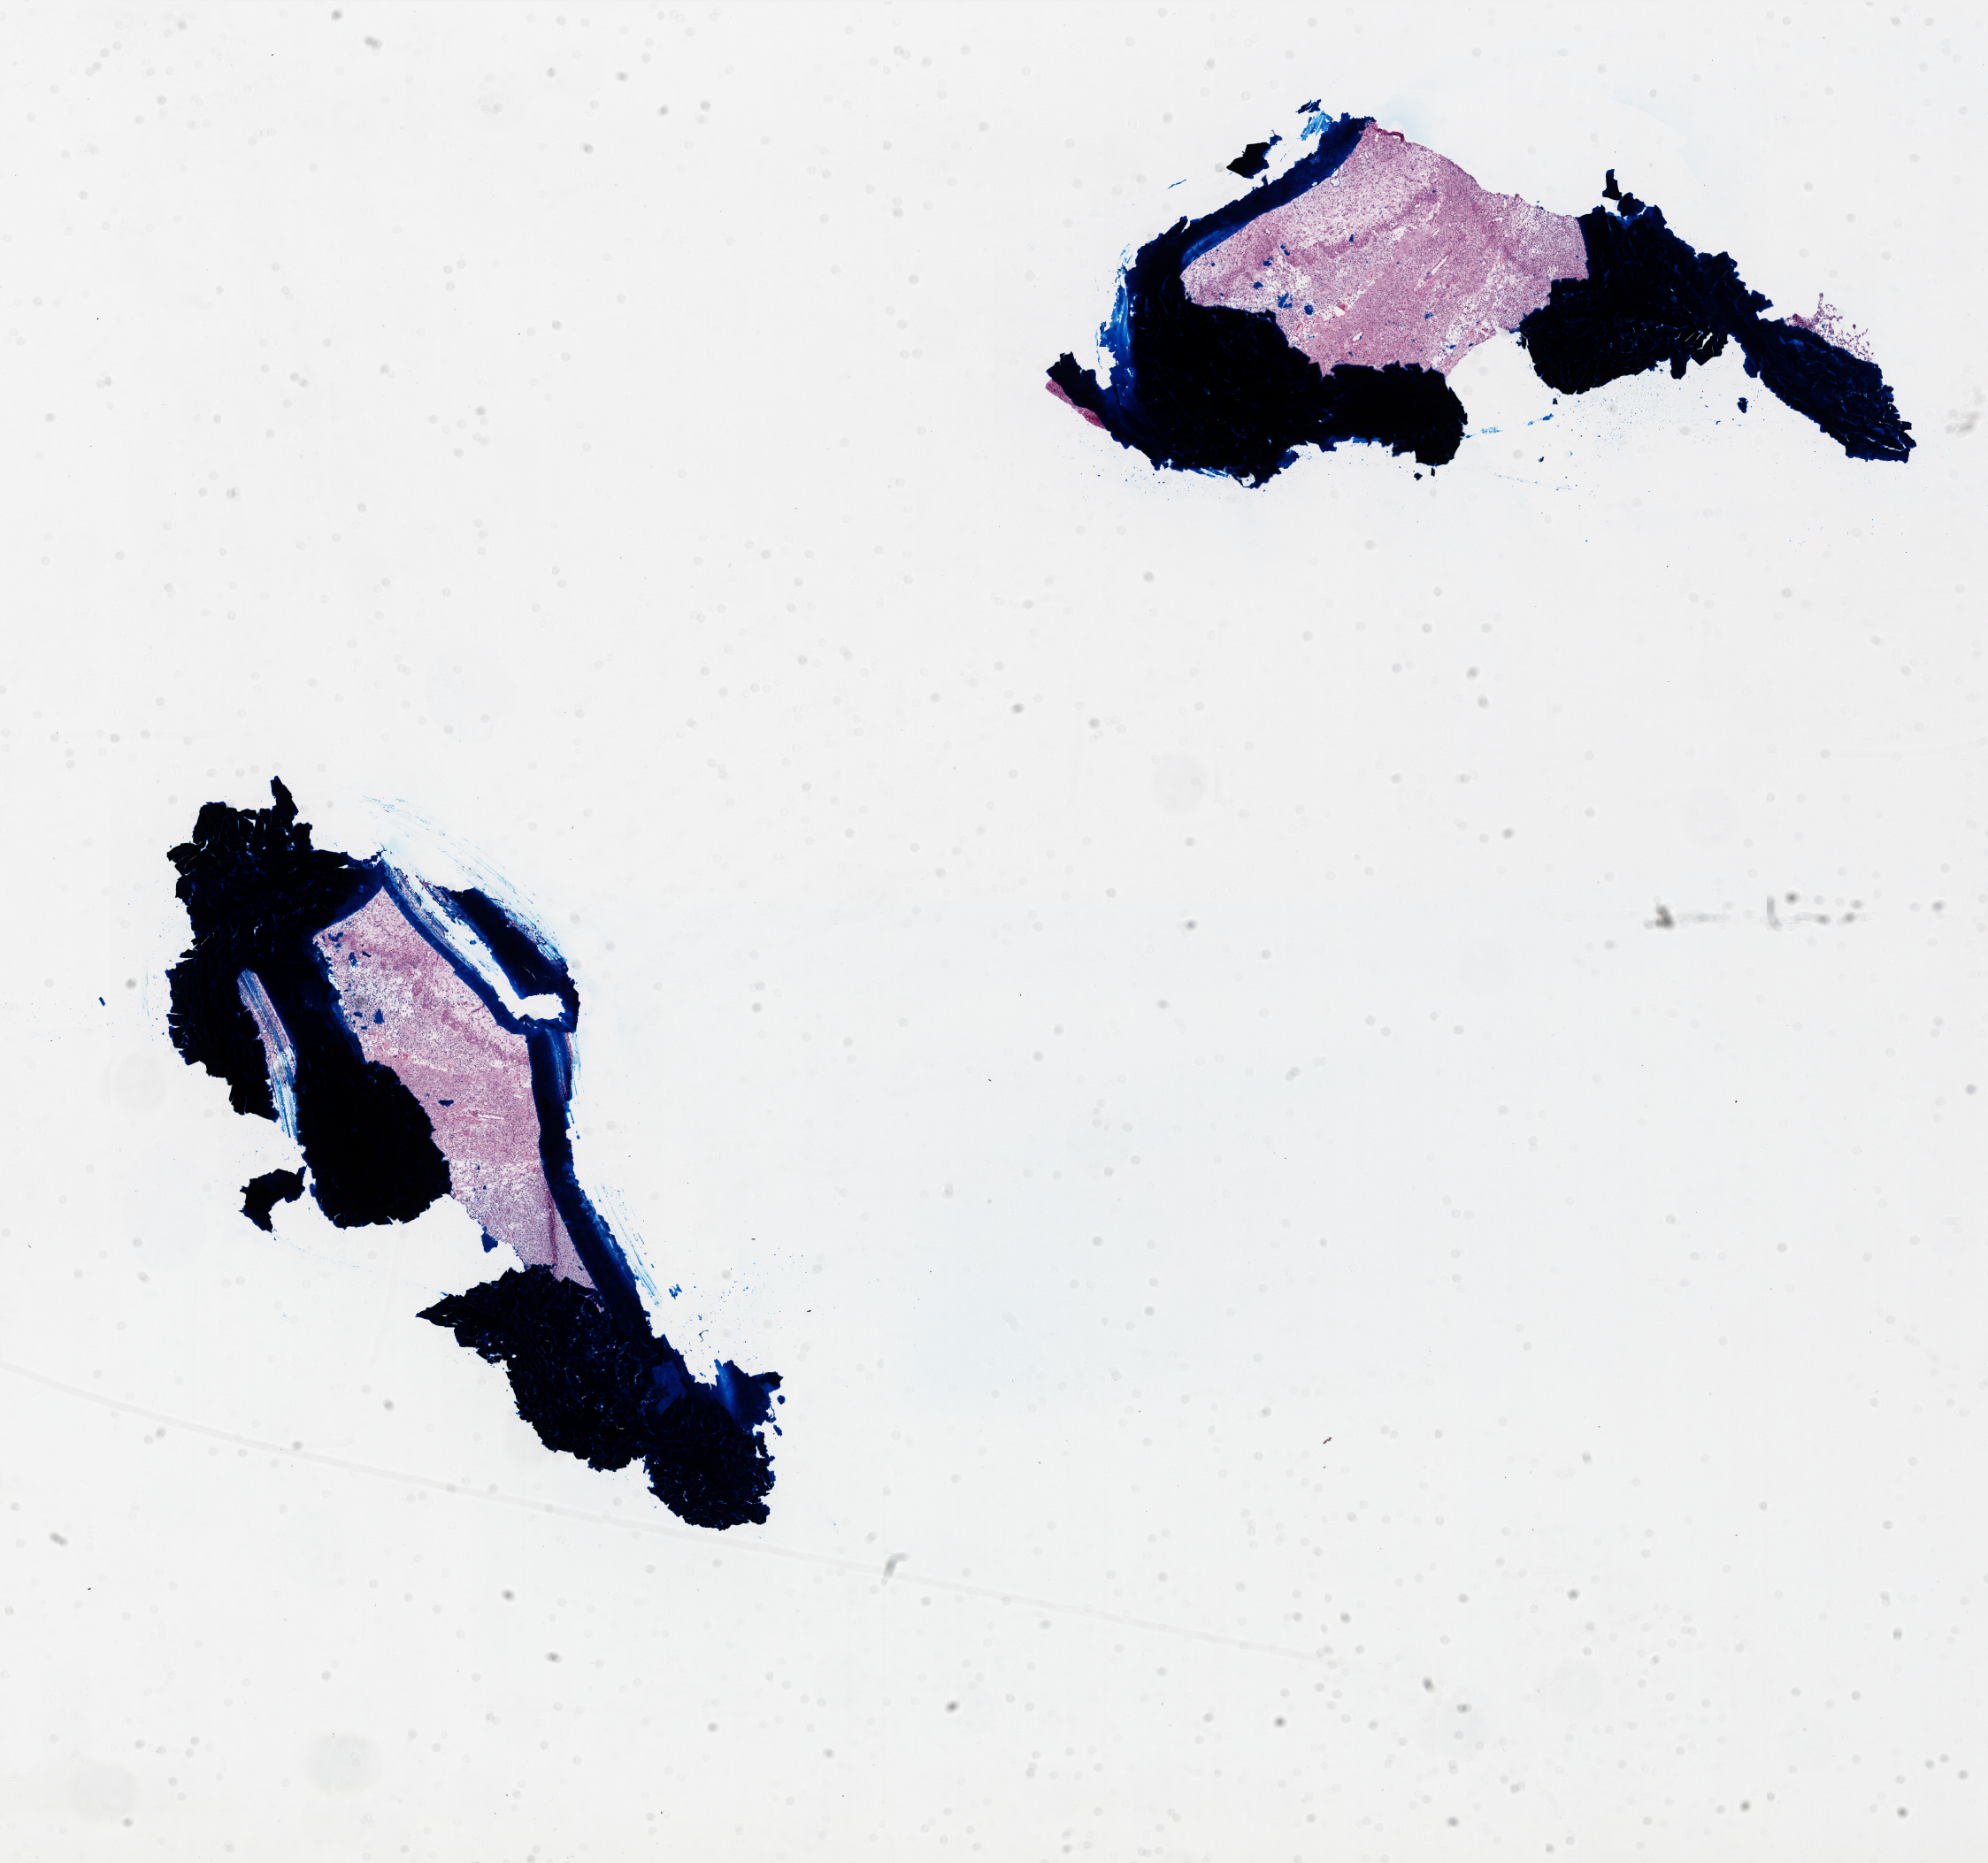
H&E whole-slide image — a low-resolution overview of the entire scanned area, about 18.0 x 16.9 mm (slide scanned at 20x), frozen section from the top of the tissue portion, sample: primary tumour, brain. Patient: male, age at initial diagnosis 47 years. Pathologist review of this section (percent, as recorded): tumour cells 90%, tumour nuclei 100%, normal cells 0%, stromal cells 0%, necrosis 10%.
Histologic diagnosis: Glioblastoma.